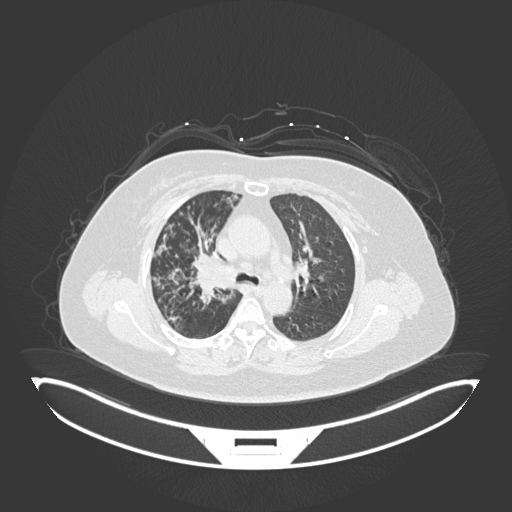
Chest CT, one axial slice; slice 121 of 245 in the series (ordered by position); reconstruction kernel B30f; lung window (W 1500 / L -600 HU); 1 mm slice thickness; 512 × 512 image matrix, field of view 500 × 500 mm. Patient: female, 60 years. From the clinical record (not read from this slice): clinical TNM (as recorded): T1c N0 M0.
Structures marked on this image (bounding box drawn by a radiologist):
- lung tumour (recorded histology: squamous cell carcinoma): bounding box (x1, y1, x2, y2) in pixels: (190, 253, 240, 294)